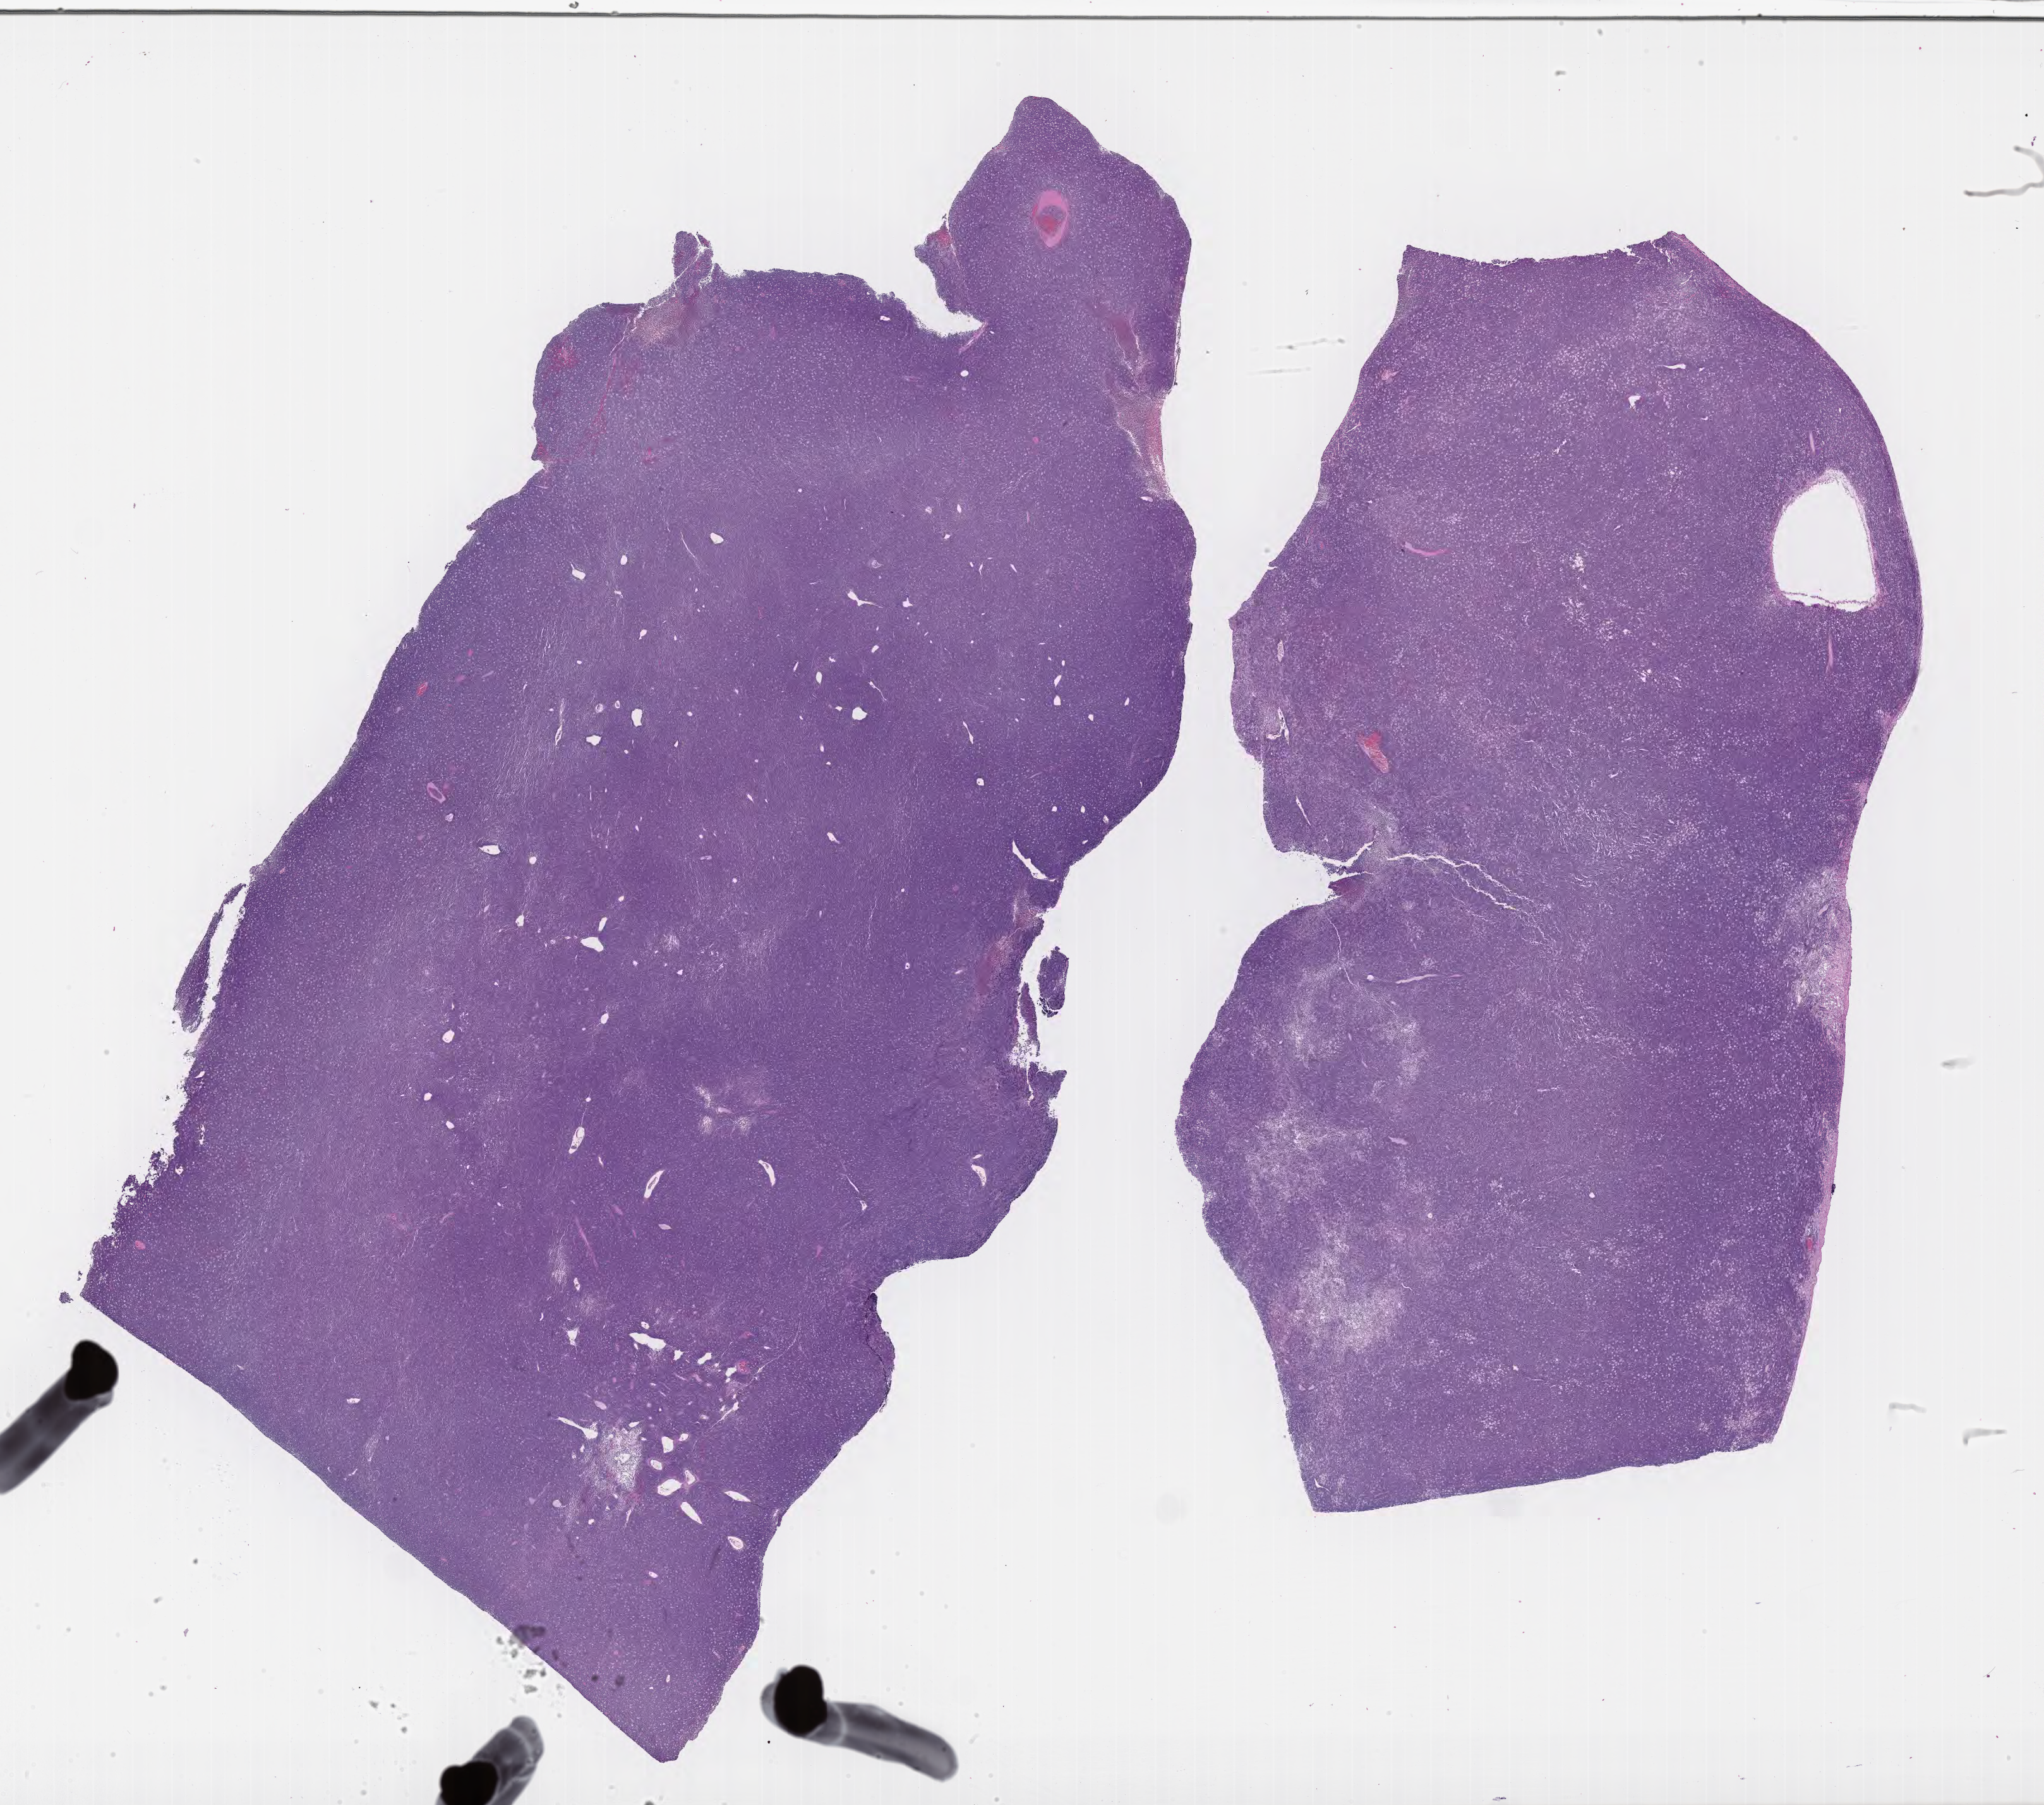
H&E whole-slide image, whole scanned area (about 26.2 x 23.1 mm) shown as a low-resolution overview; specimen: tumor tissue. Female patient, aged 34.
• histologic diagnosis: Burkitt lymphoma, NOS